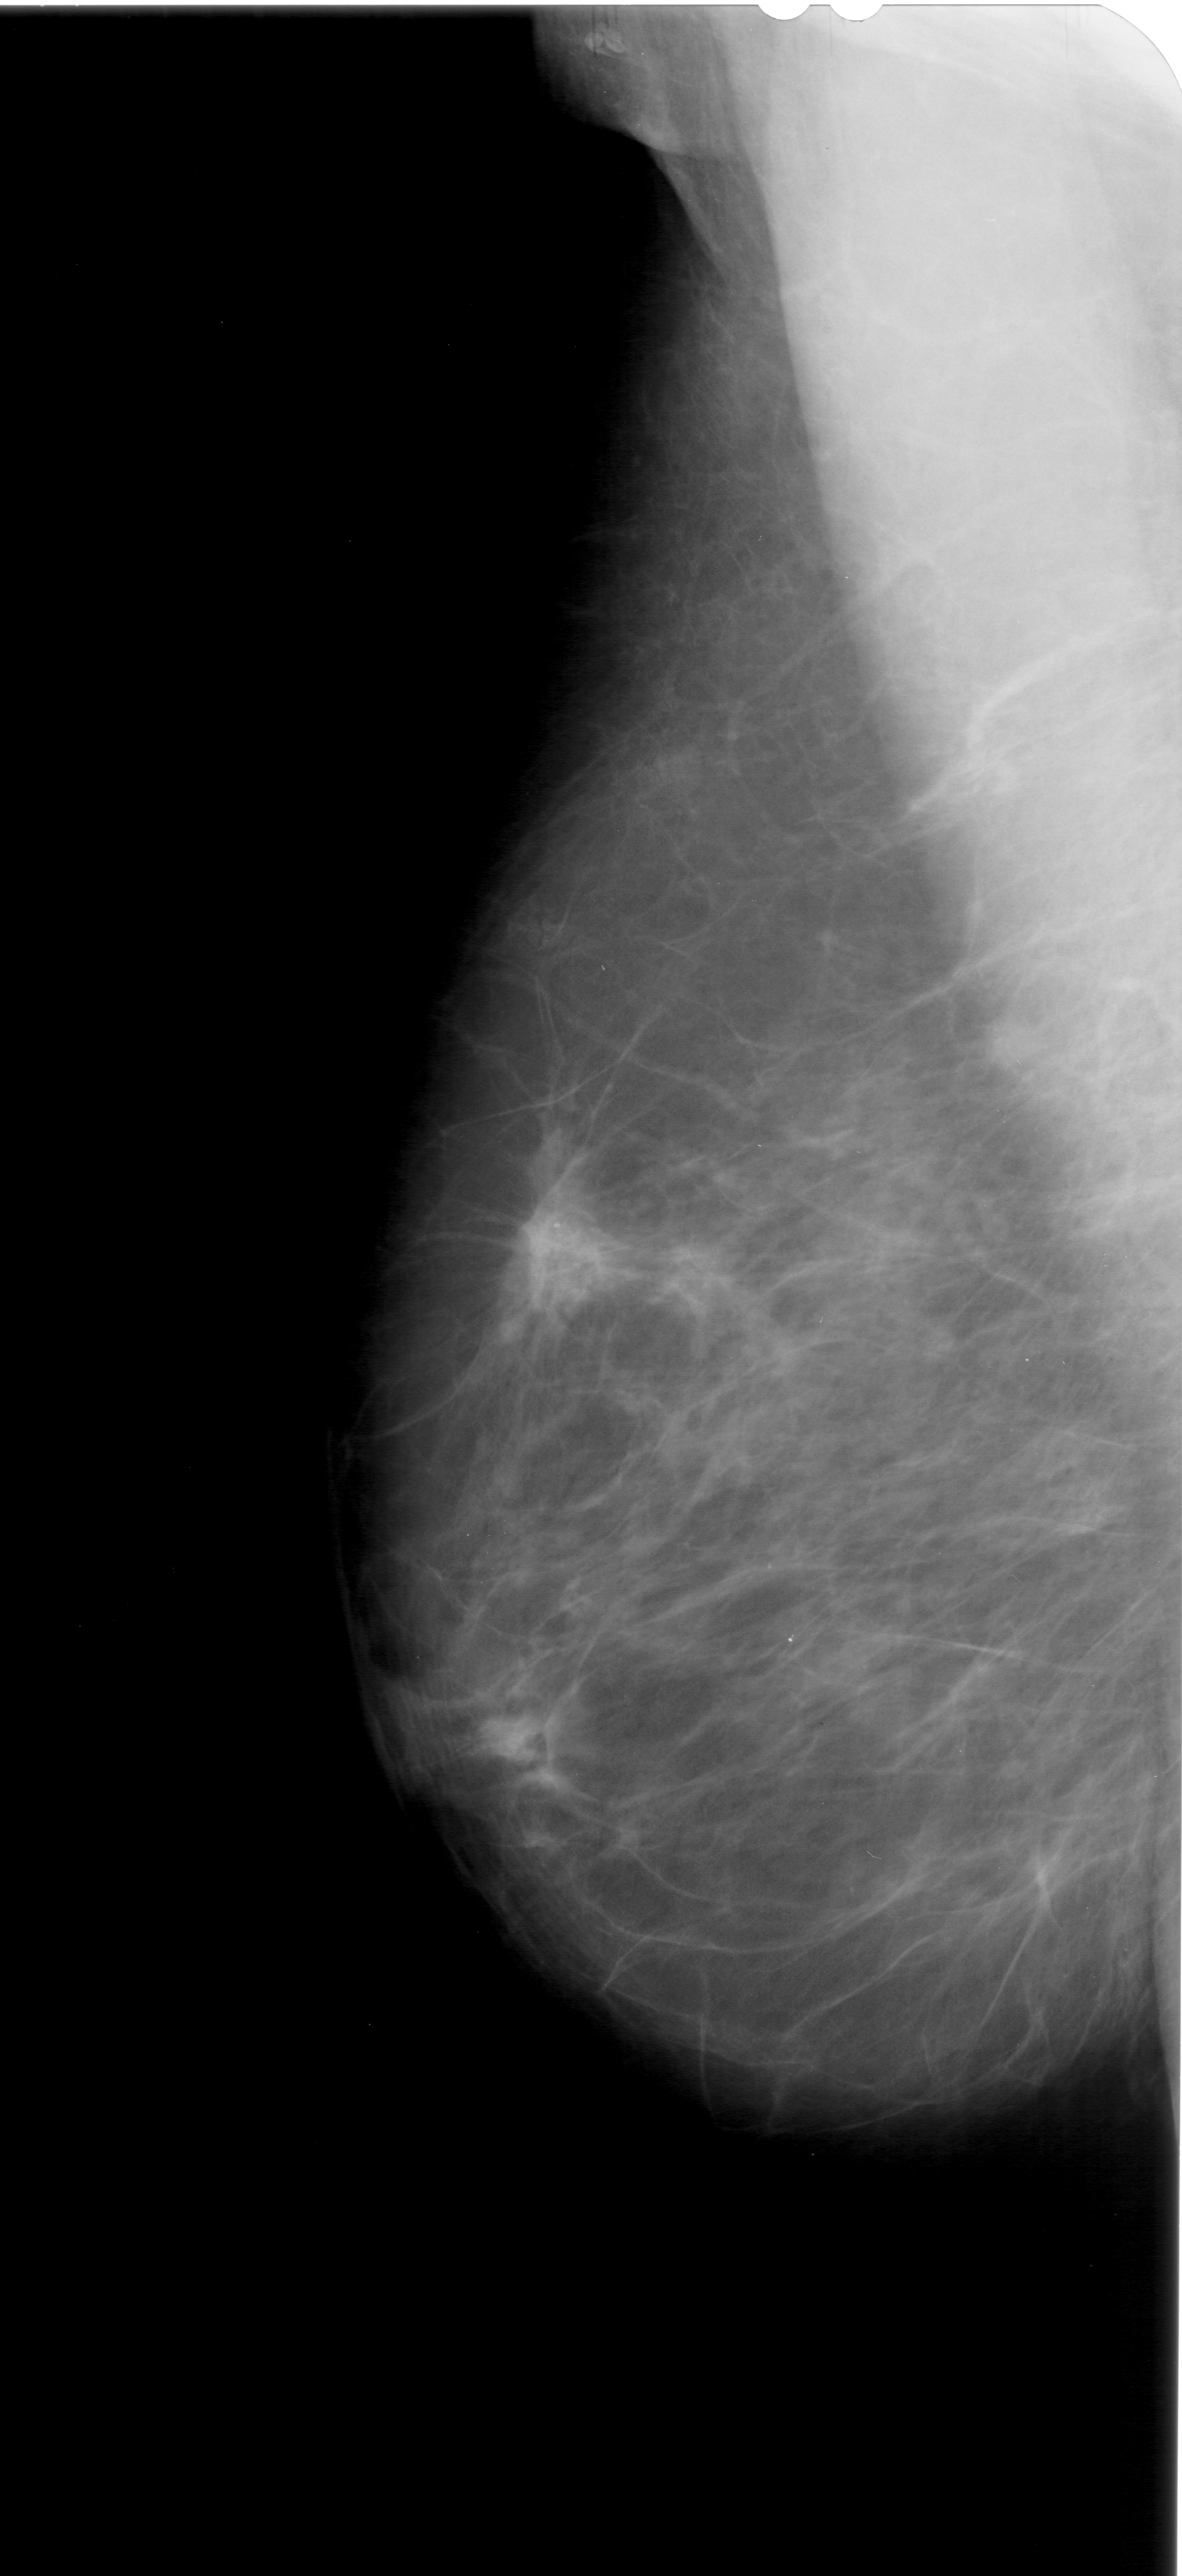
Scanned film-screen mammogram. Left breast. Mediolateral oblique (MLO) view. 1182 × 2576 image matrix.
Marked abnormalities (boxes around the expert regions of interest):
- mass, shape irregular, margins spiculated; BI-RADS assessment category 5; pathology result (as recorded, not read from the image): malignant: bounding box [x1, y1, x2, y2] px = [460, 1160, 624, 1321]